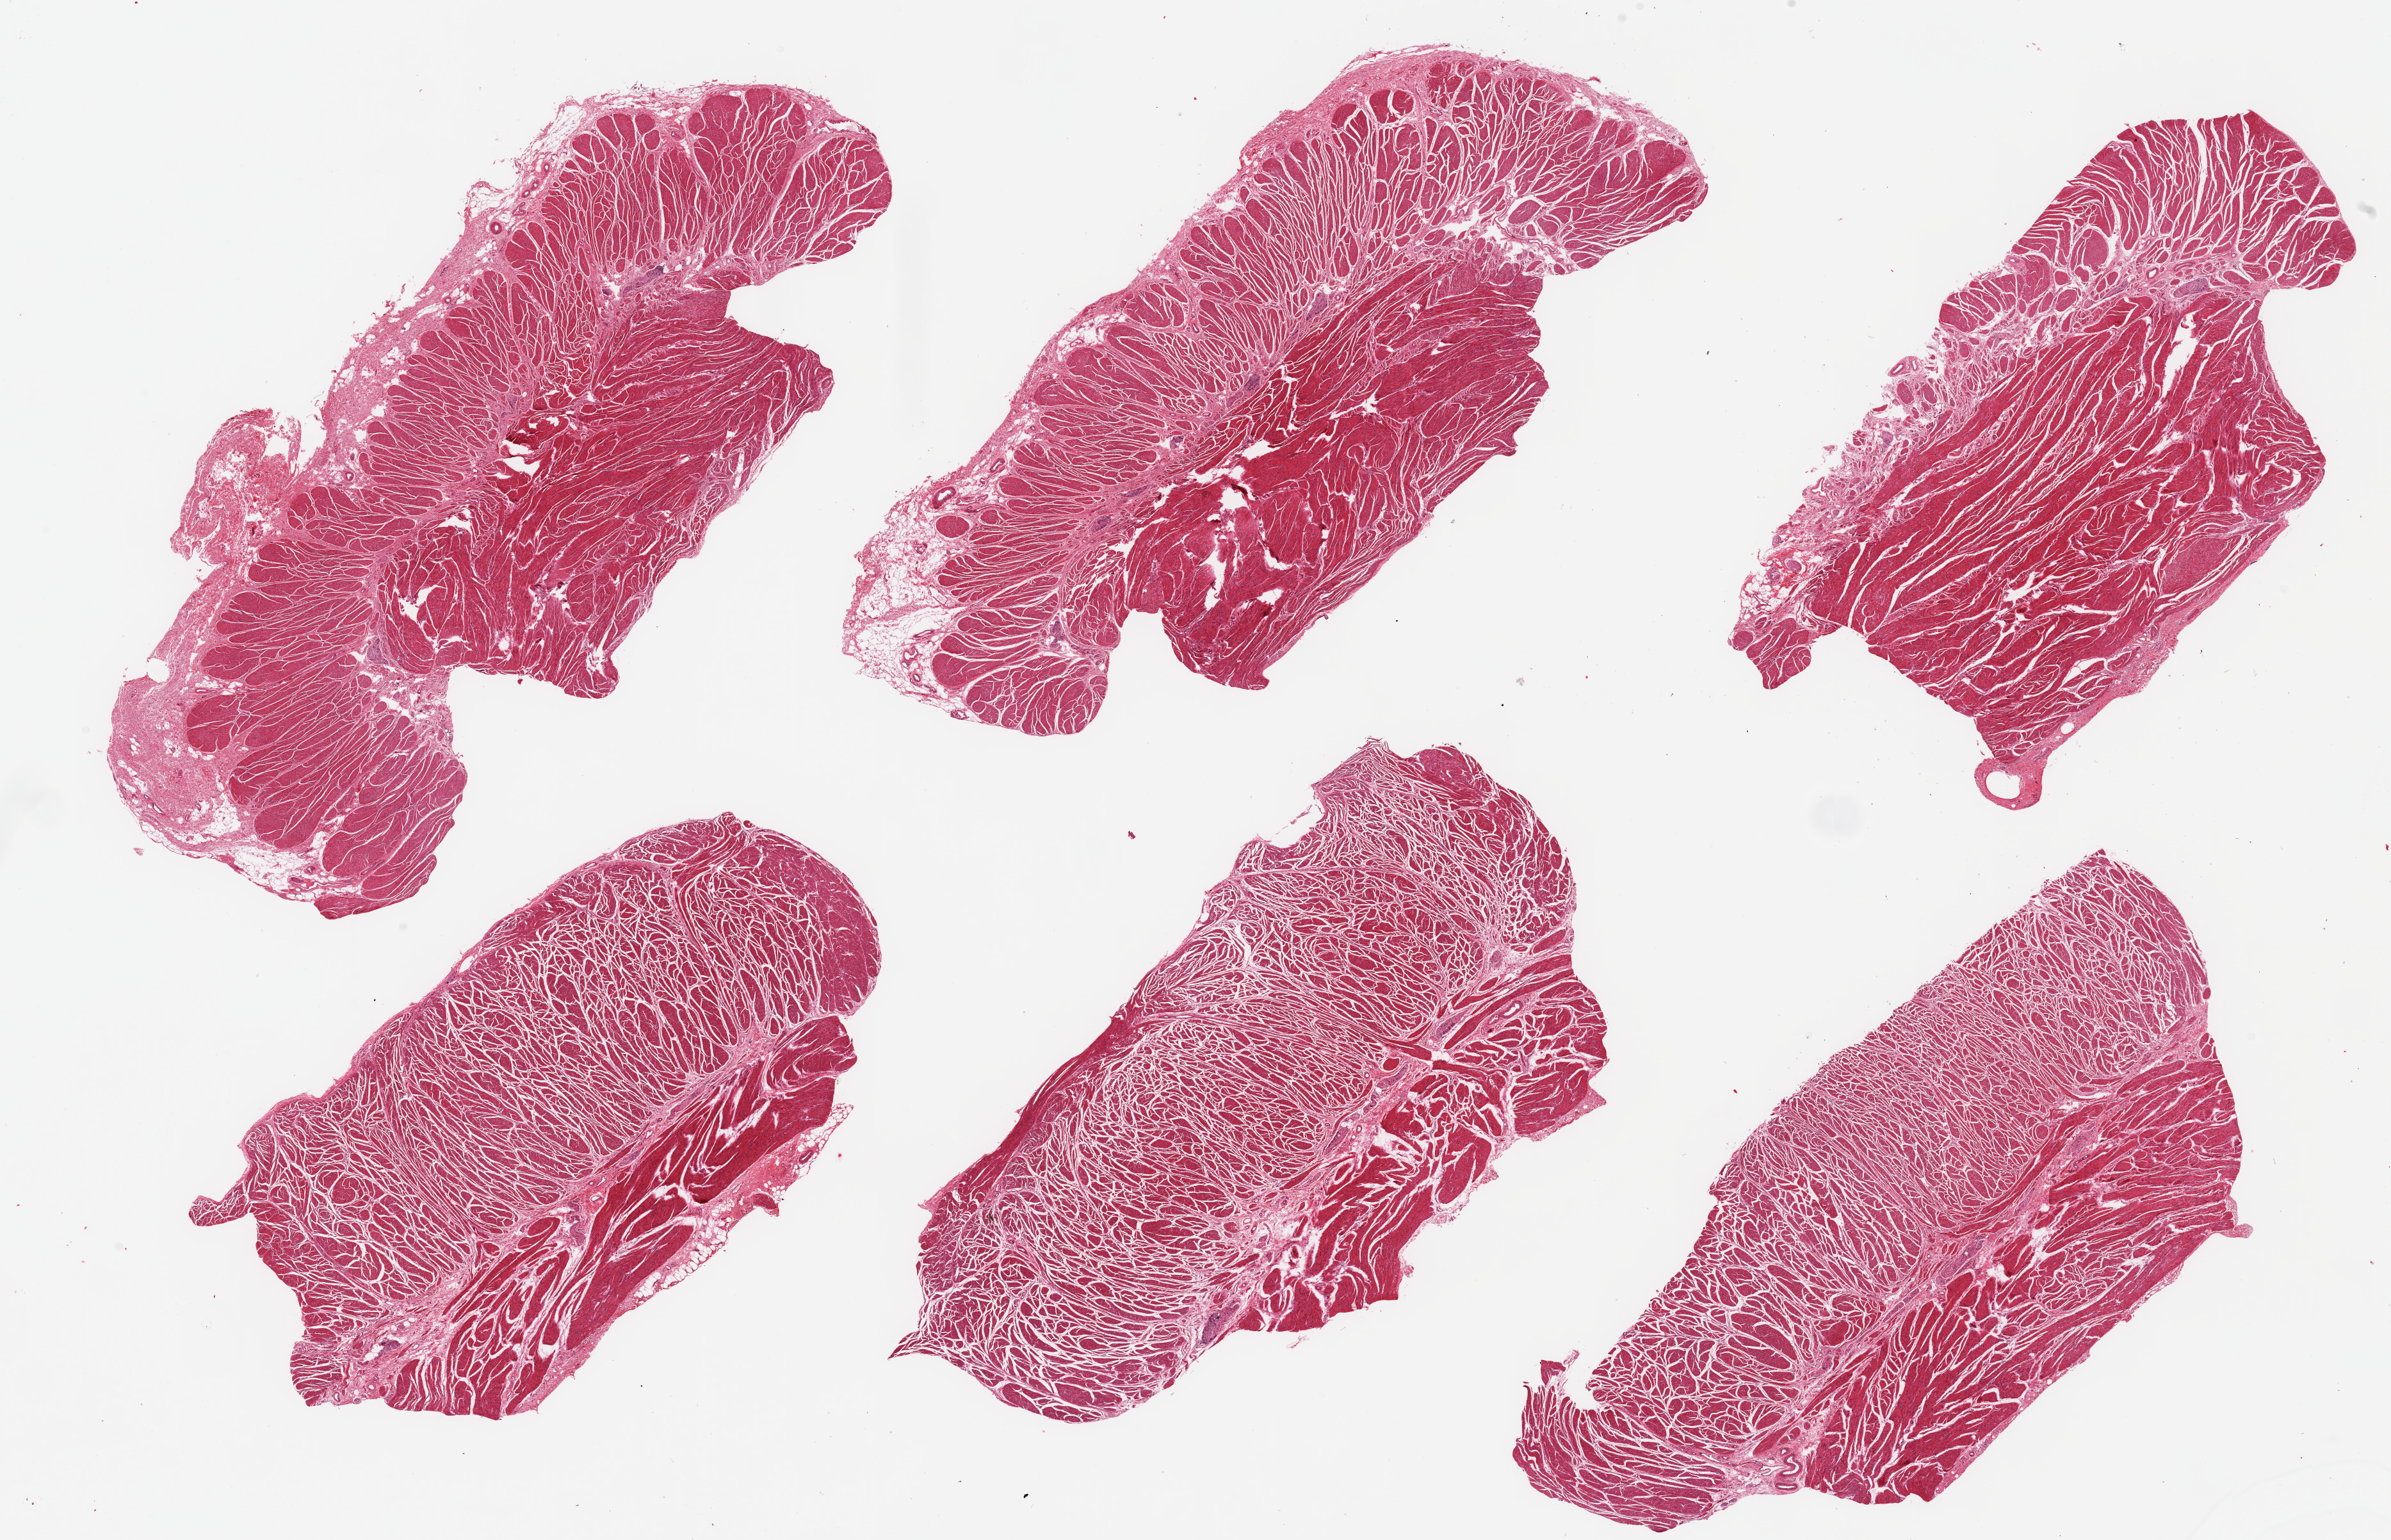
Haematoxylin and eosin whole-slide image, brightfield — shown as a low-resolution overview of the whole scanned area (about 29.5 x 19.0 mm, slide scanned at 20x). PAXgene-fixed, paraffin-embedded tissue. Target tissue: gastroesophageal junction. Donor tissue sample. Donor sex: male.
Pathologist's review note for this sample: 6 pieces, confirmed target muscularis.